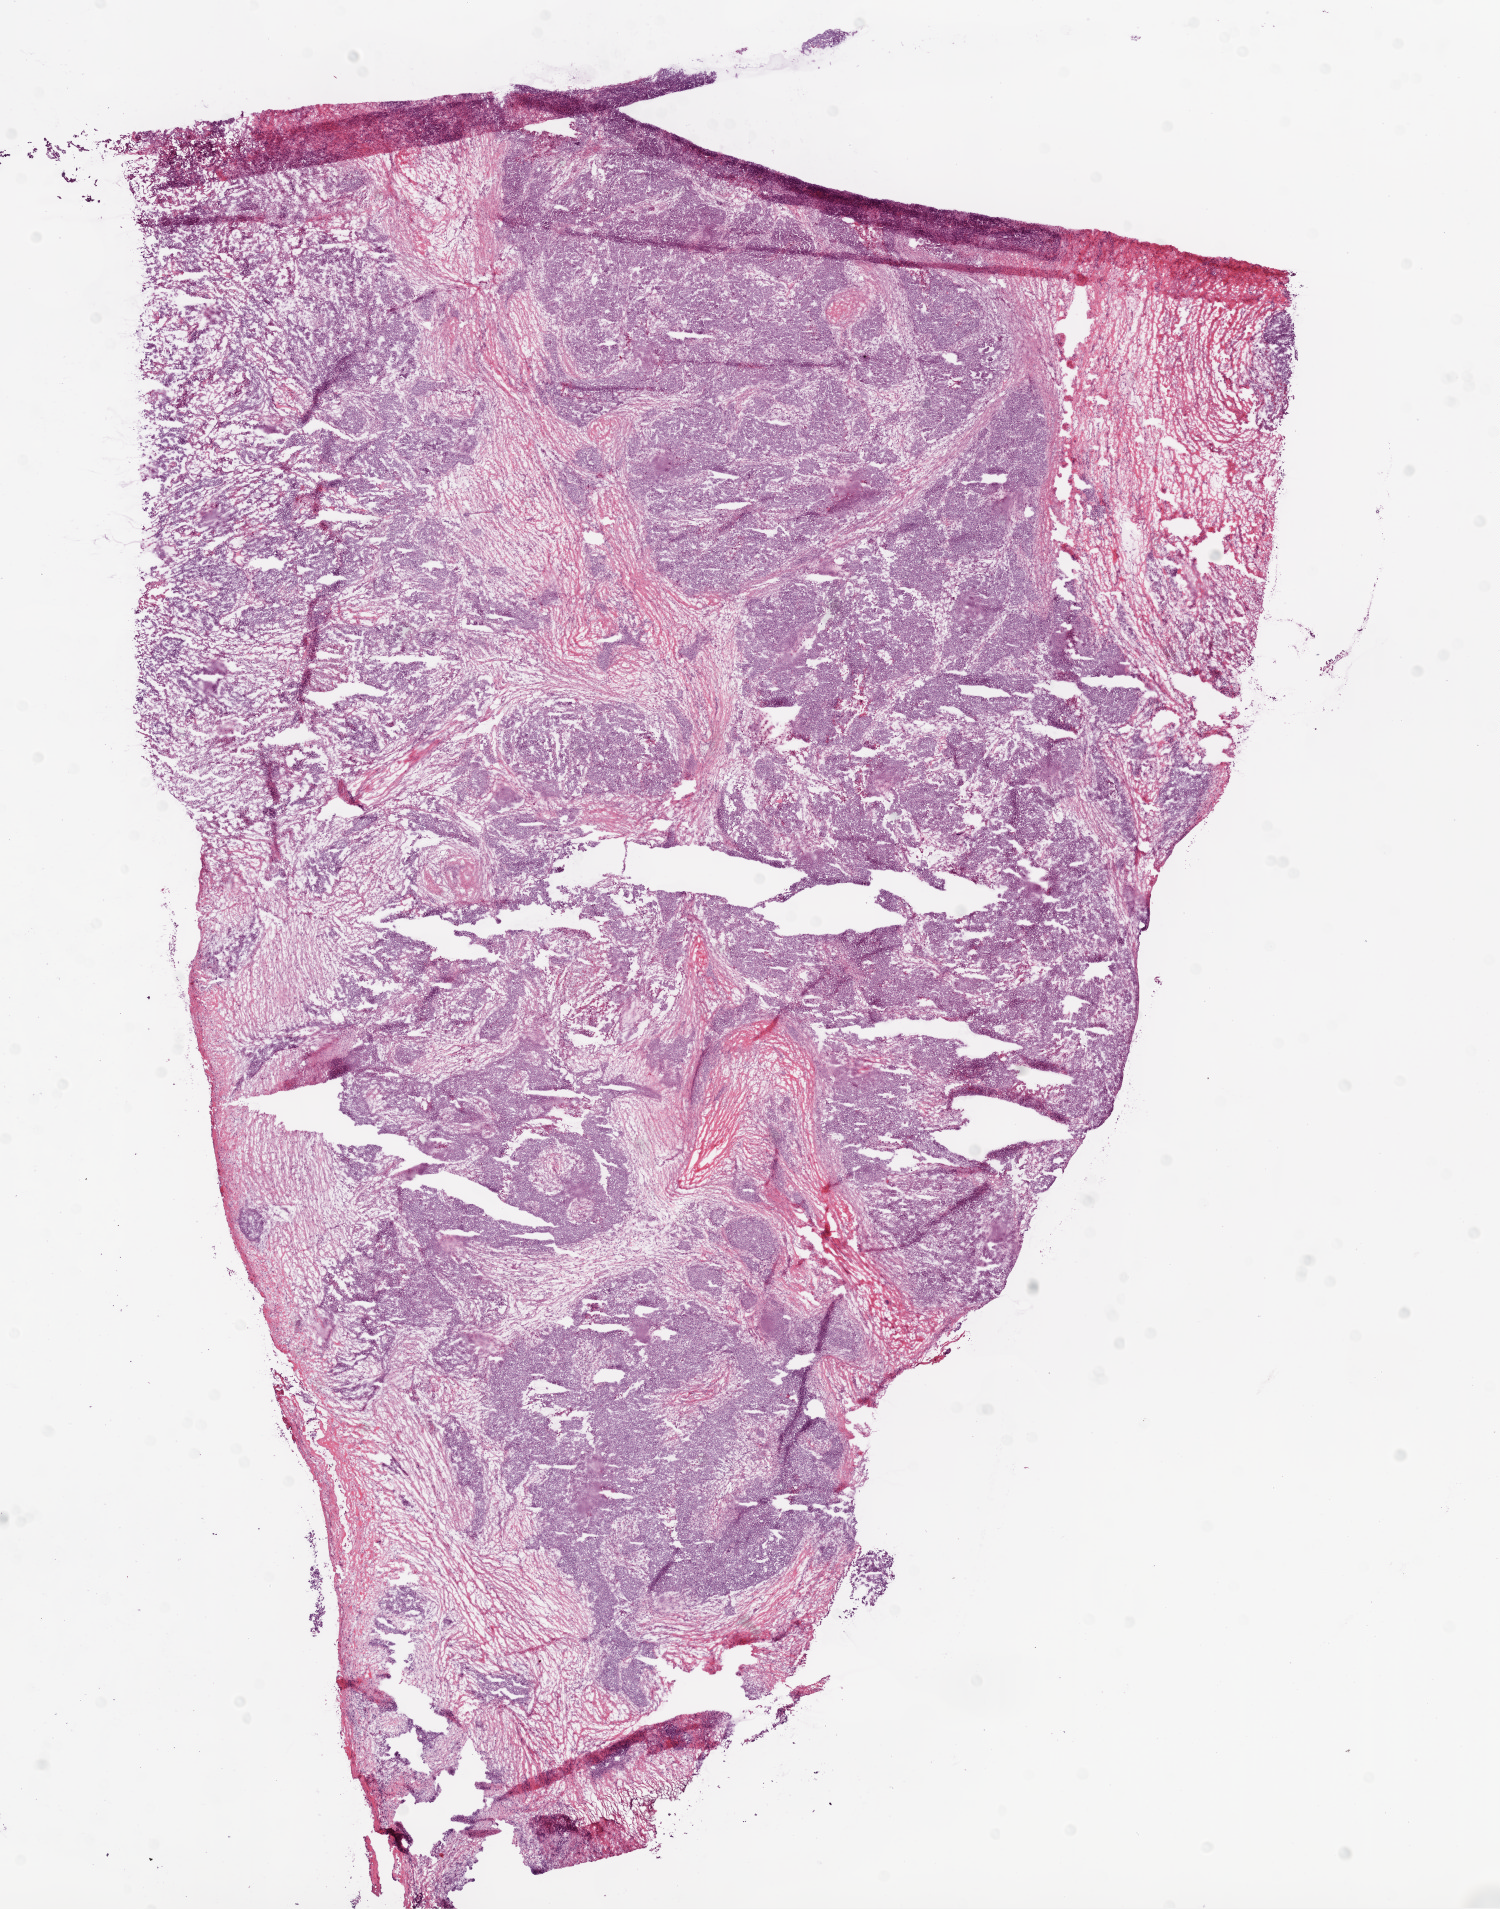
Digitized Hematoxylin and eosin (H&E) stained tissue section (whole slide), shown as a low-resolution overview of the whole scanned area (about 12.0 x 15.3 mm); frozen section from the top of the tissue portion; sample: primary tumour, ovary. Female, age 58 years at initial diagnosis. Histologic grade: G2 (moderately differentiated). Pathologist review of this section (percent, as recorded): tumour cells 70%, tumour nuclei 80%, normal cells 0%, stromal cells 20%, necrosis 10%.
Laterality: bilateral. Diagnosis: Serous cystadenocarcinoma, NOS. FIGO stage: IIIC.